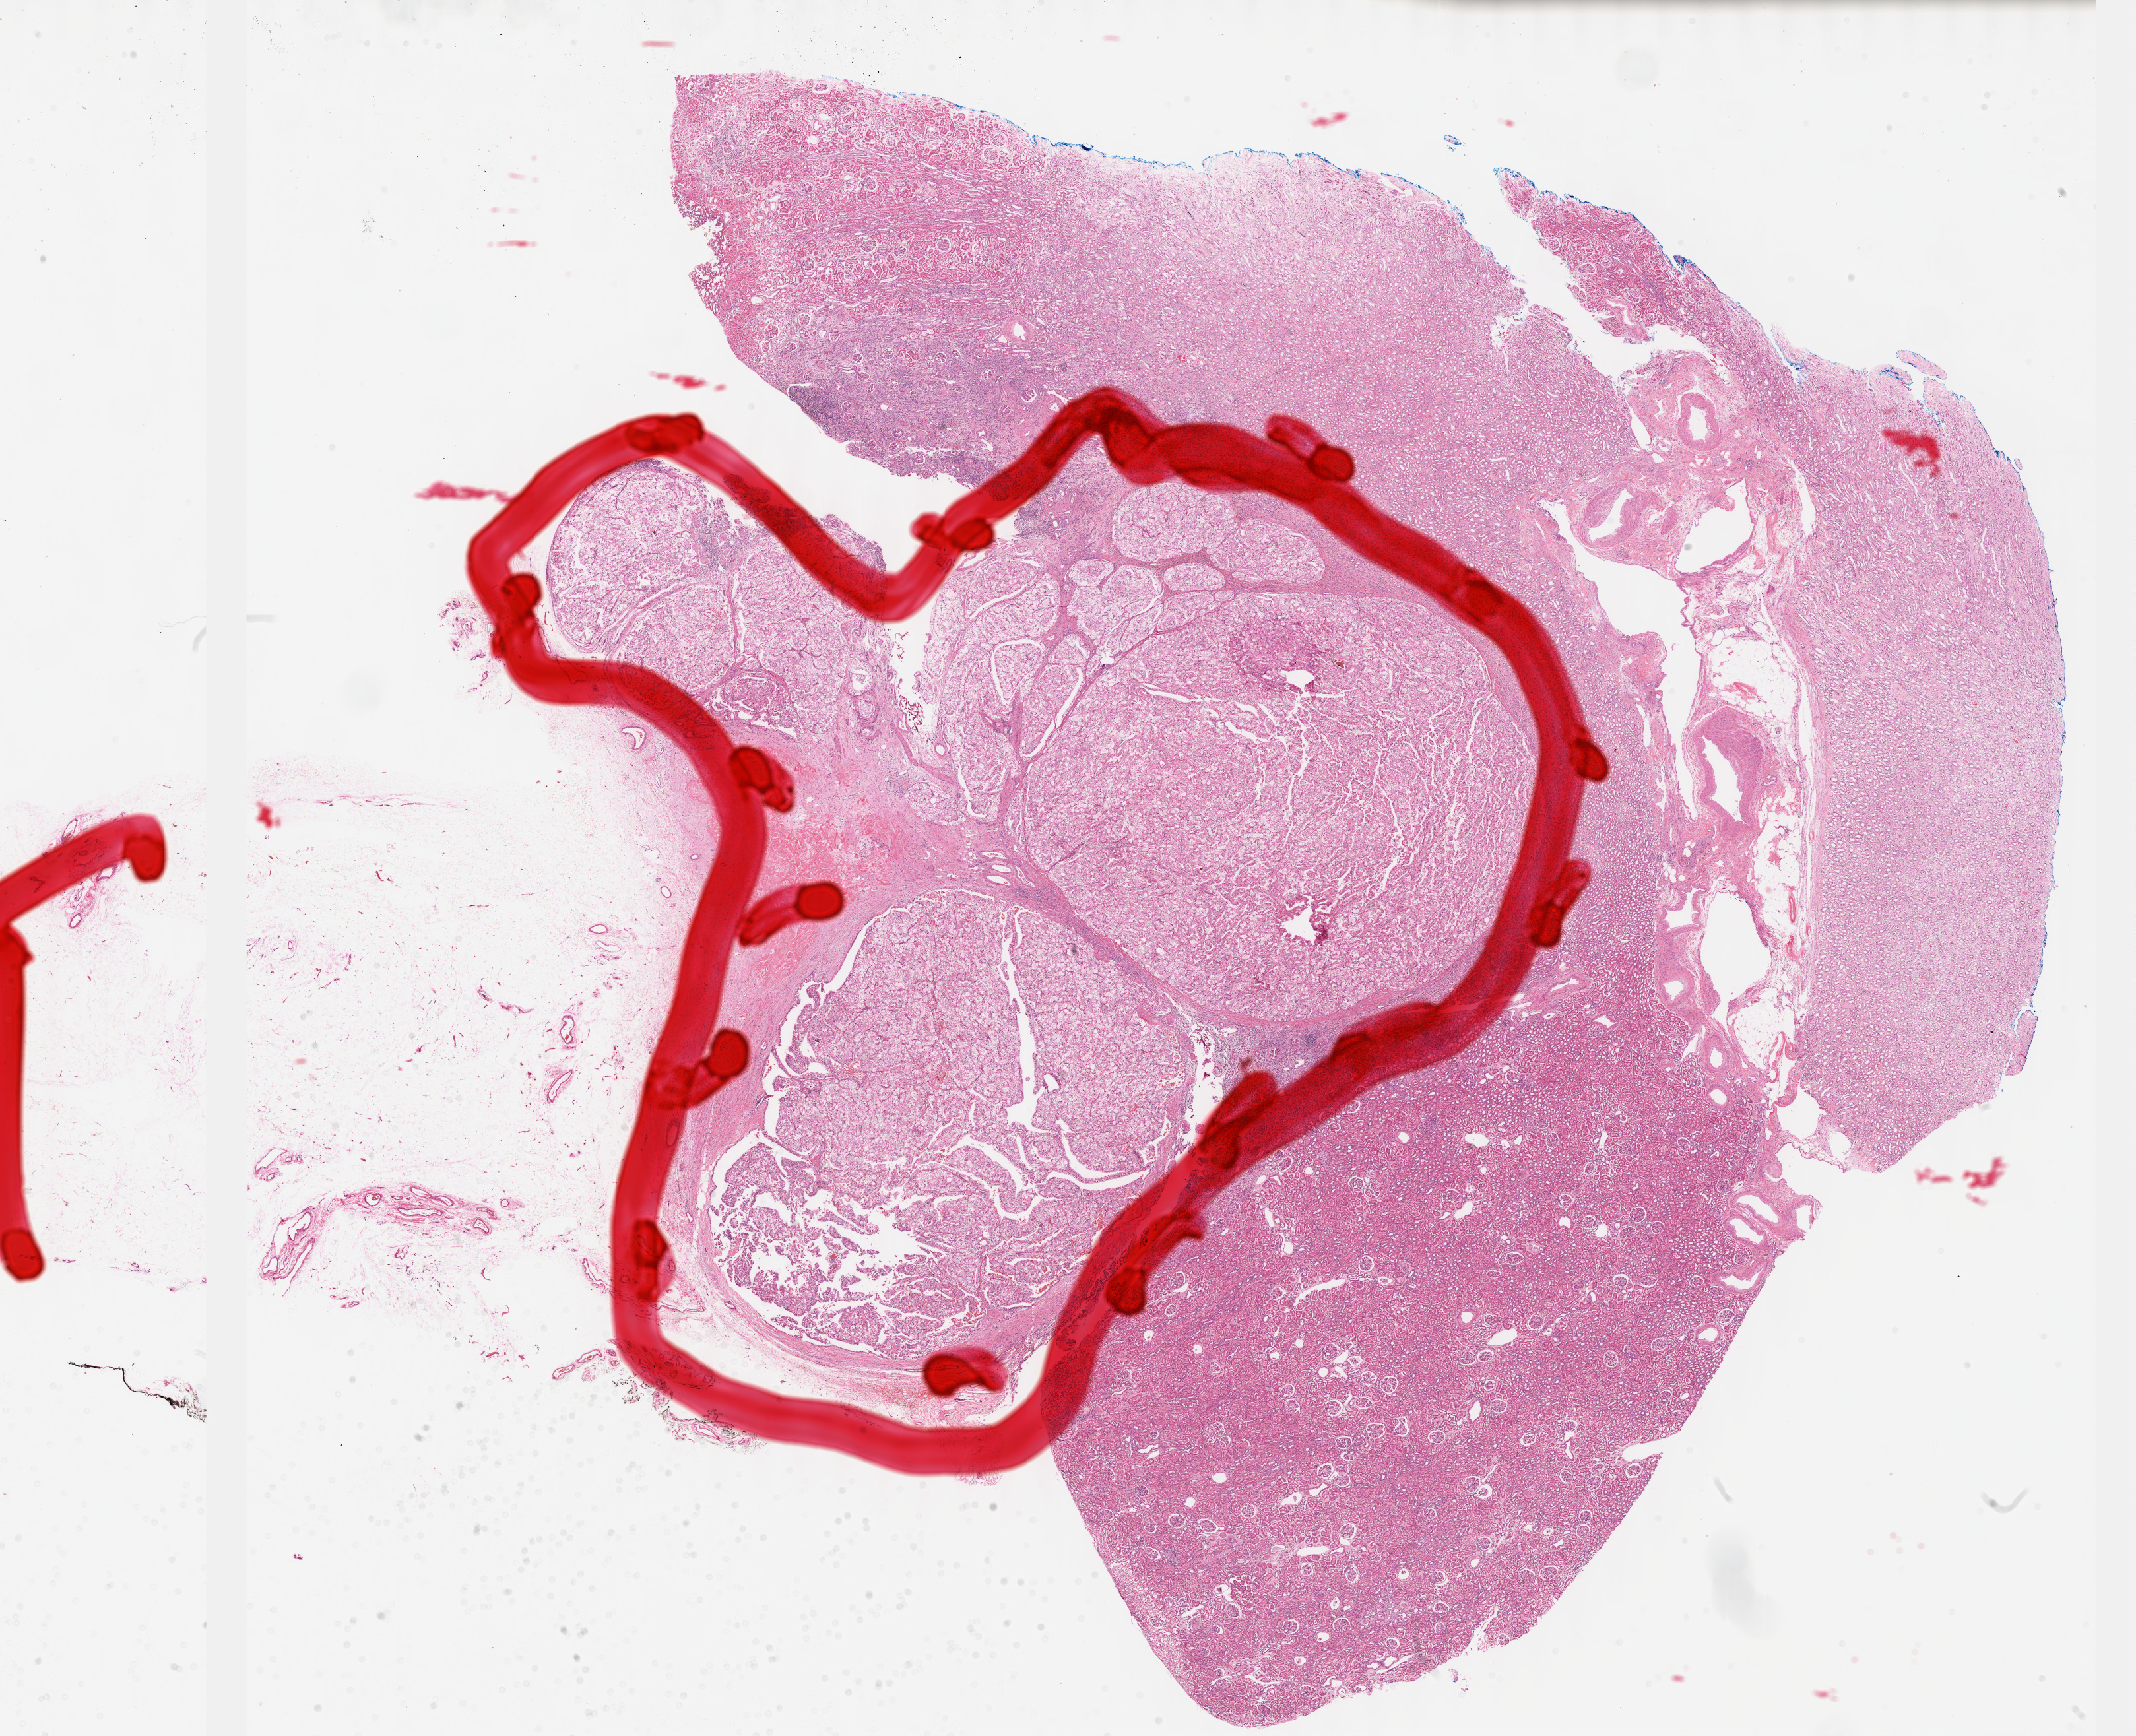
Hematoxylin and eosin (H&E) stained whole-slide image — low-resolution overview of the scanned area, about 26.2 x 21.3 mm (acquisition: 40x scan); formalin-fixed paraffin-embedded (FFPE) diagnostic section; kidney, primary tumour sample. Patient: female, age at initial diagnosis 59 years. Composition of this section per pathologist review: tumour cells 83%, tumour nuclei 88%.
Diagnosis: Renal cell carcinoma, chromophobe type.